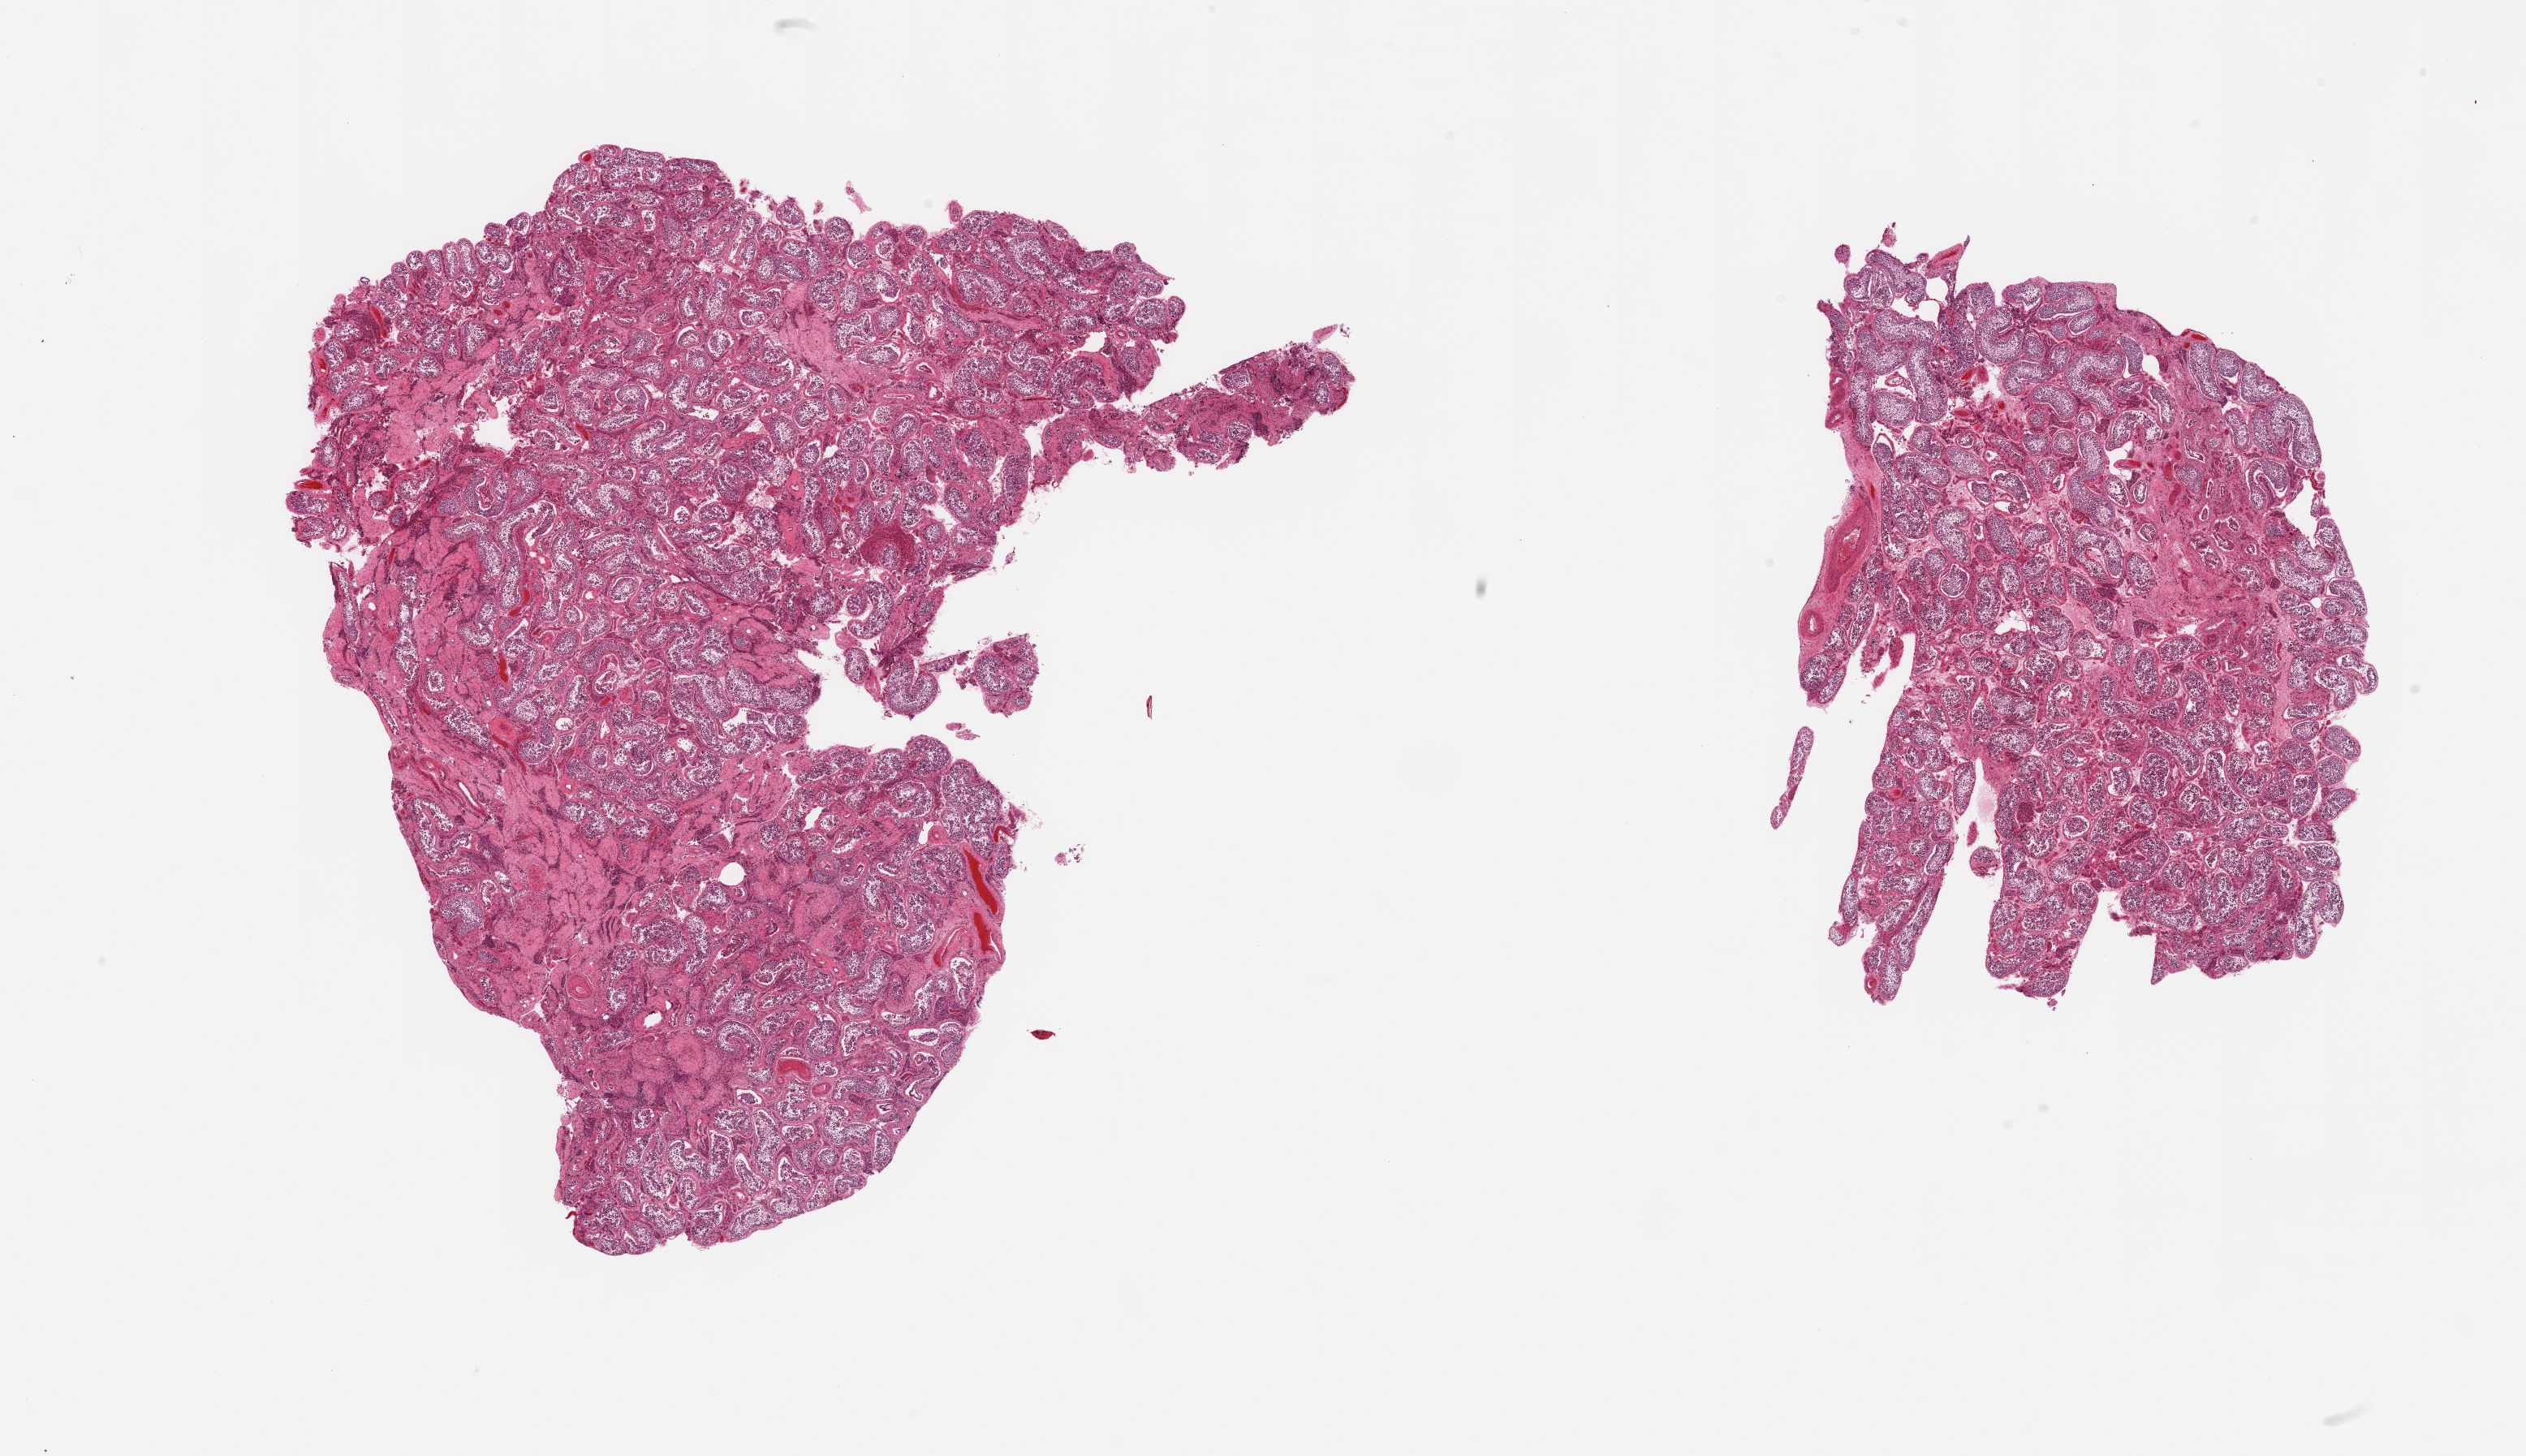
Digitized hematoxylin and eosin (H&E)-stained section — shown as a low-resolution overview of the whole scanned area (about 24.6 x 14.2 mm, acquisition: 20x scan). PAXgene-fixed paraffin-embedded (PFPE) section. Target tissue: testis. Donor tissue sample. Donor sex: male.
* pathologist's review note for this sample: 2 pieces; spermatogenesis; focus of hyalinized tubules comprises 20% of 1 piece